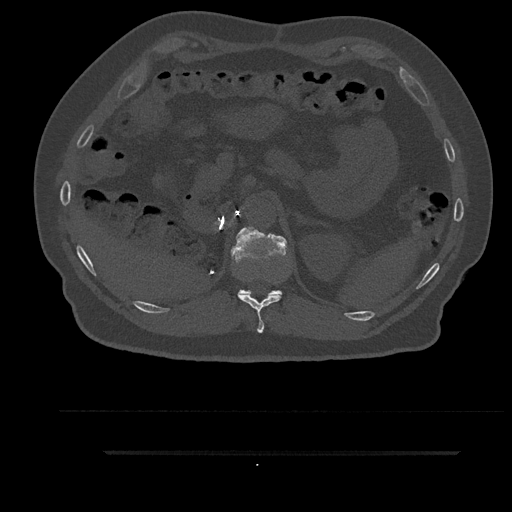
CT including the spine, one axial slice; slice 276 of 797 in the series (ordered by position); 120 kVp; bone window (W 1800 / L 400 HU); 0.5 mm slice thickness; 512 × 512 image matrix, field of view 432 × 432 mm. Patient: male, 63 years. Case-level facts recorded for this patient, not image findings: primary cancer: renal.
Outlined on this slice (semi-automatic segmentation, software-assisted and operator-edited):
- T11 vertebra: box from (x=238, y=278) to (x=282, y=334) px
- T12 vertebra: (x=231, y=226)–(x=287, y=295)